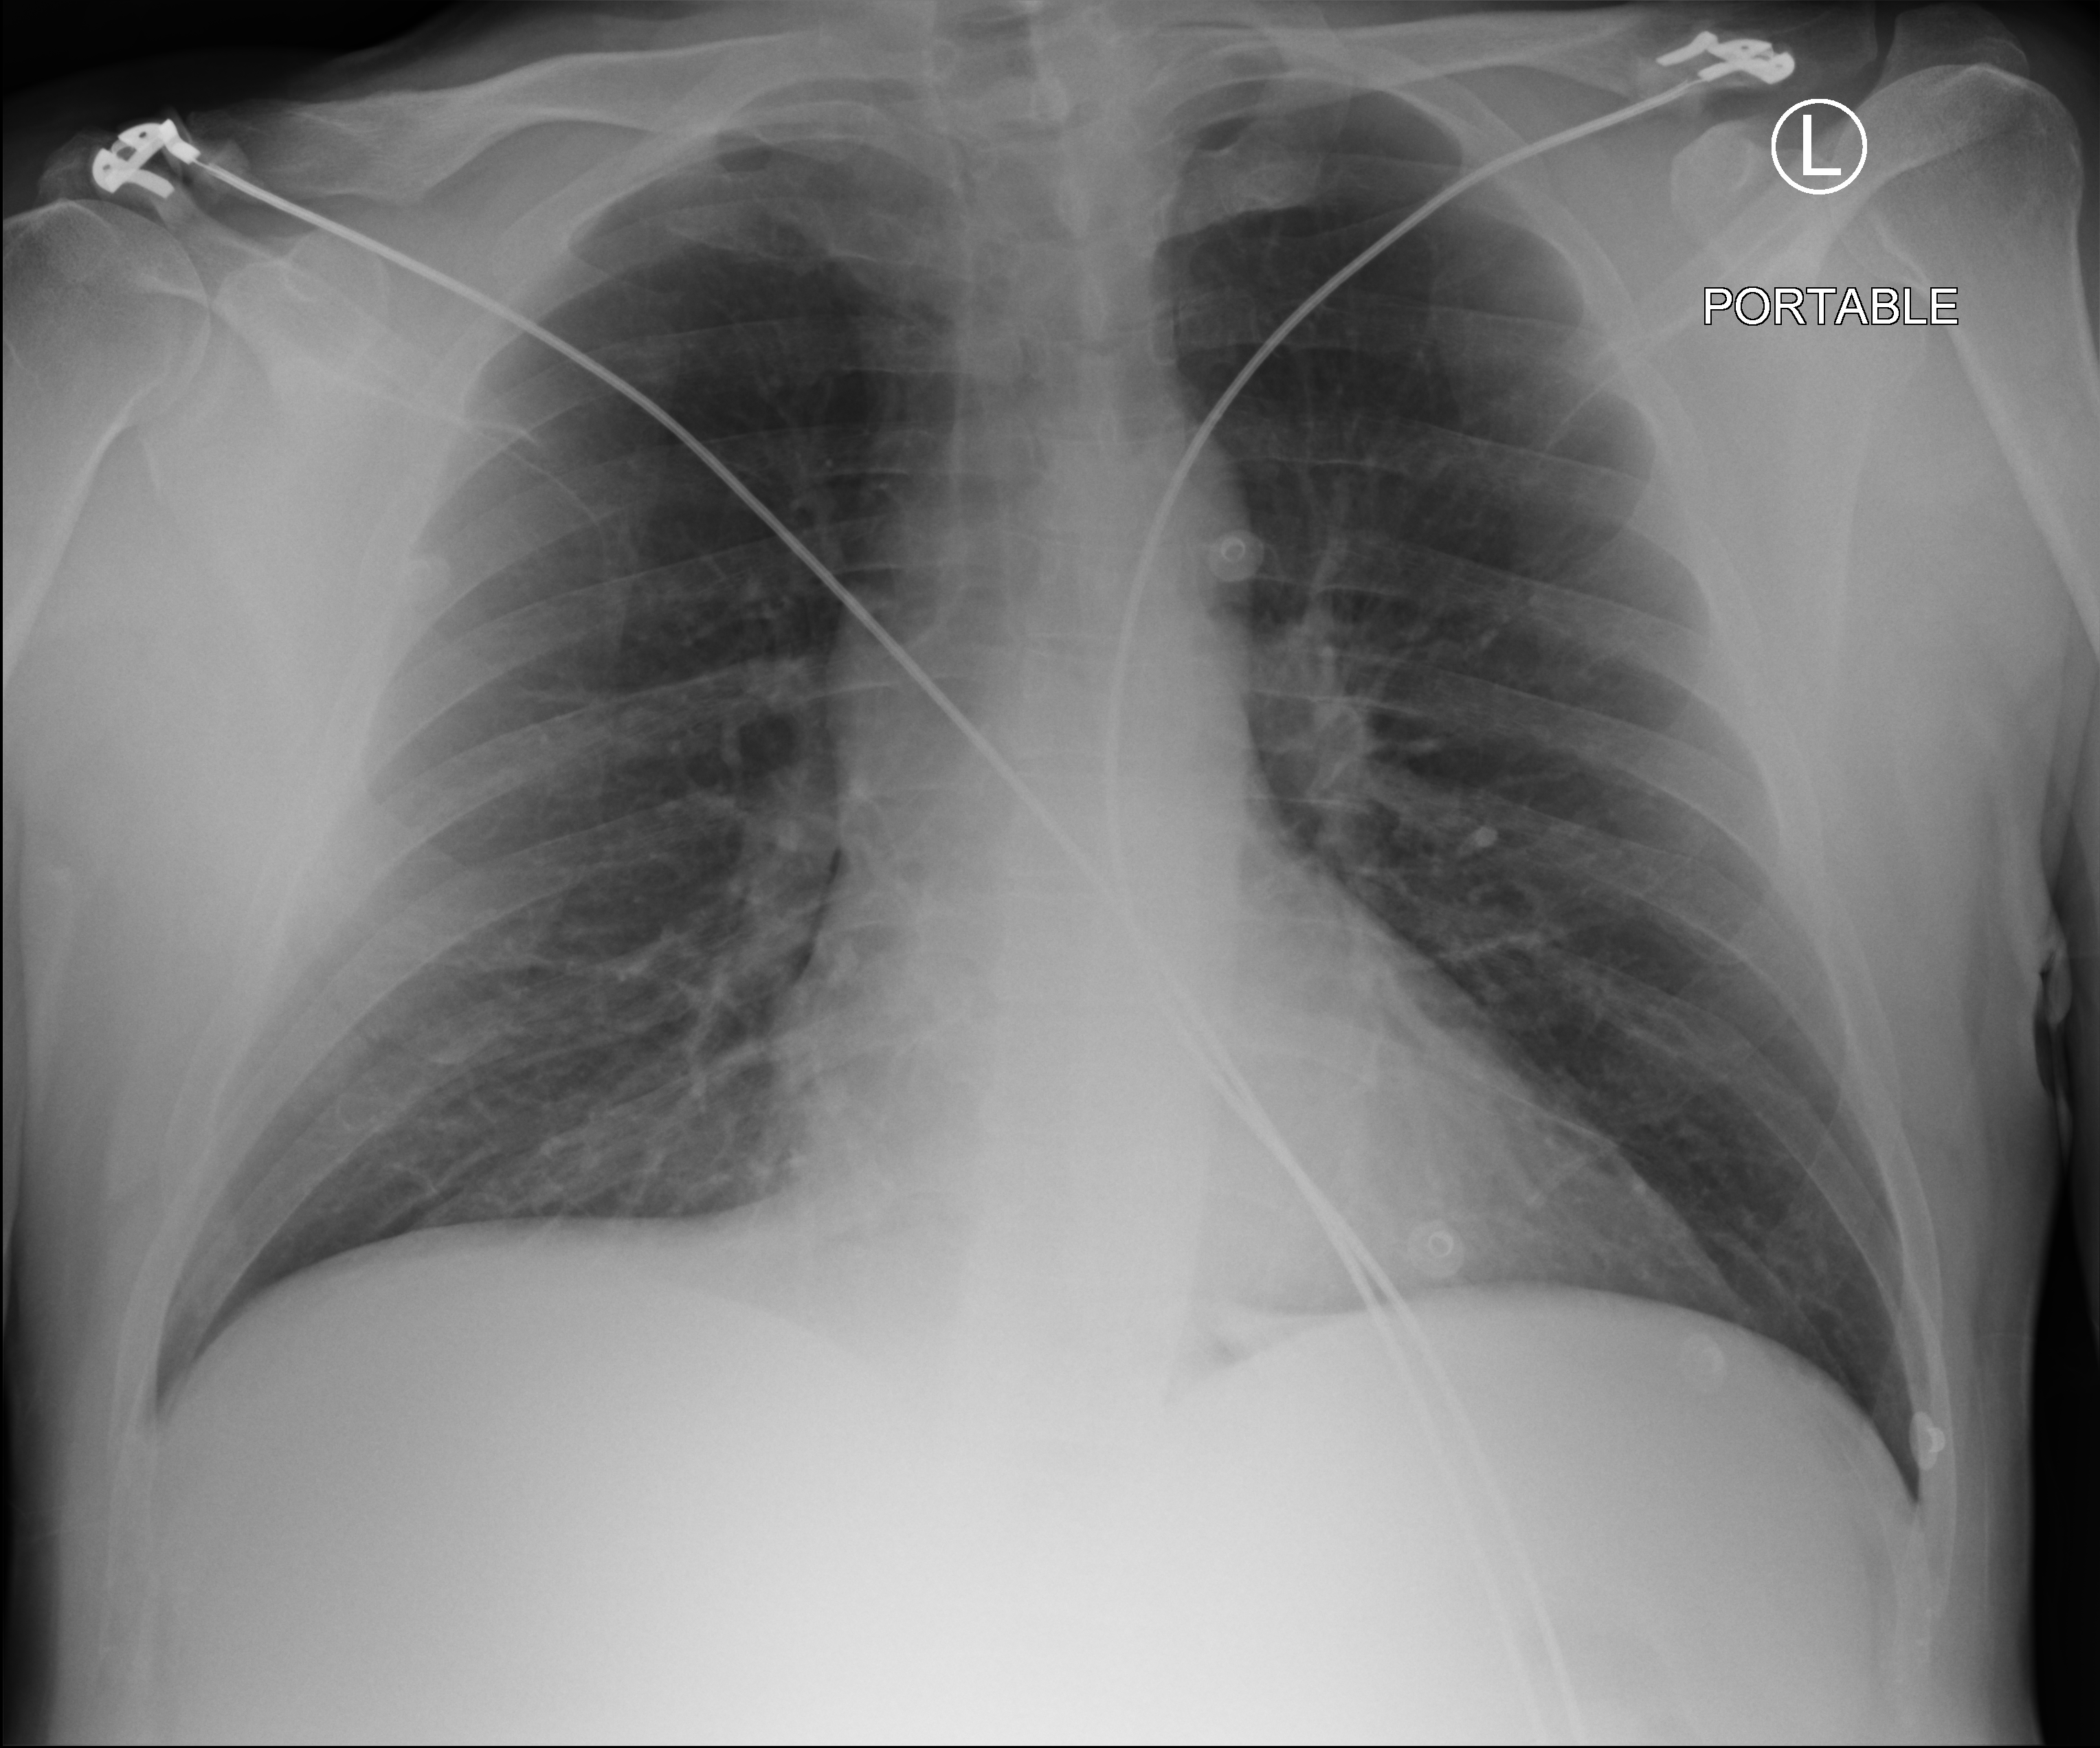
Bedside chest radiograph (computed radiography), anteroposterior (AP) projection. Patient hospitalised with COVID-19; male, aged 18–59 years.
From the hospital-stay record, not from the radiograph (when in the stay this image was taken is not recorded):
- admitted to intensive care during this hospital stay: no
- mechanically ventilated during this hospital stay: no